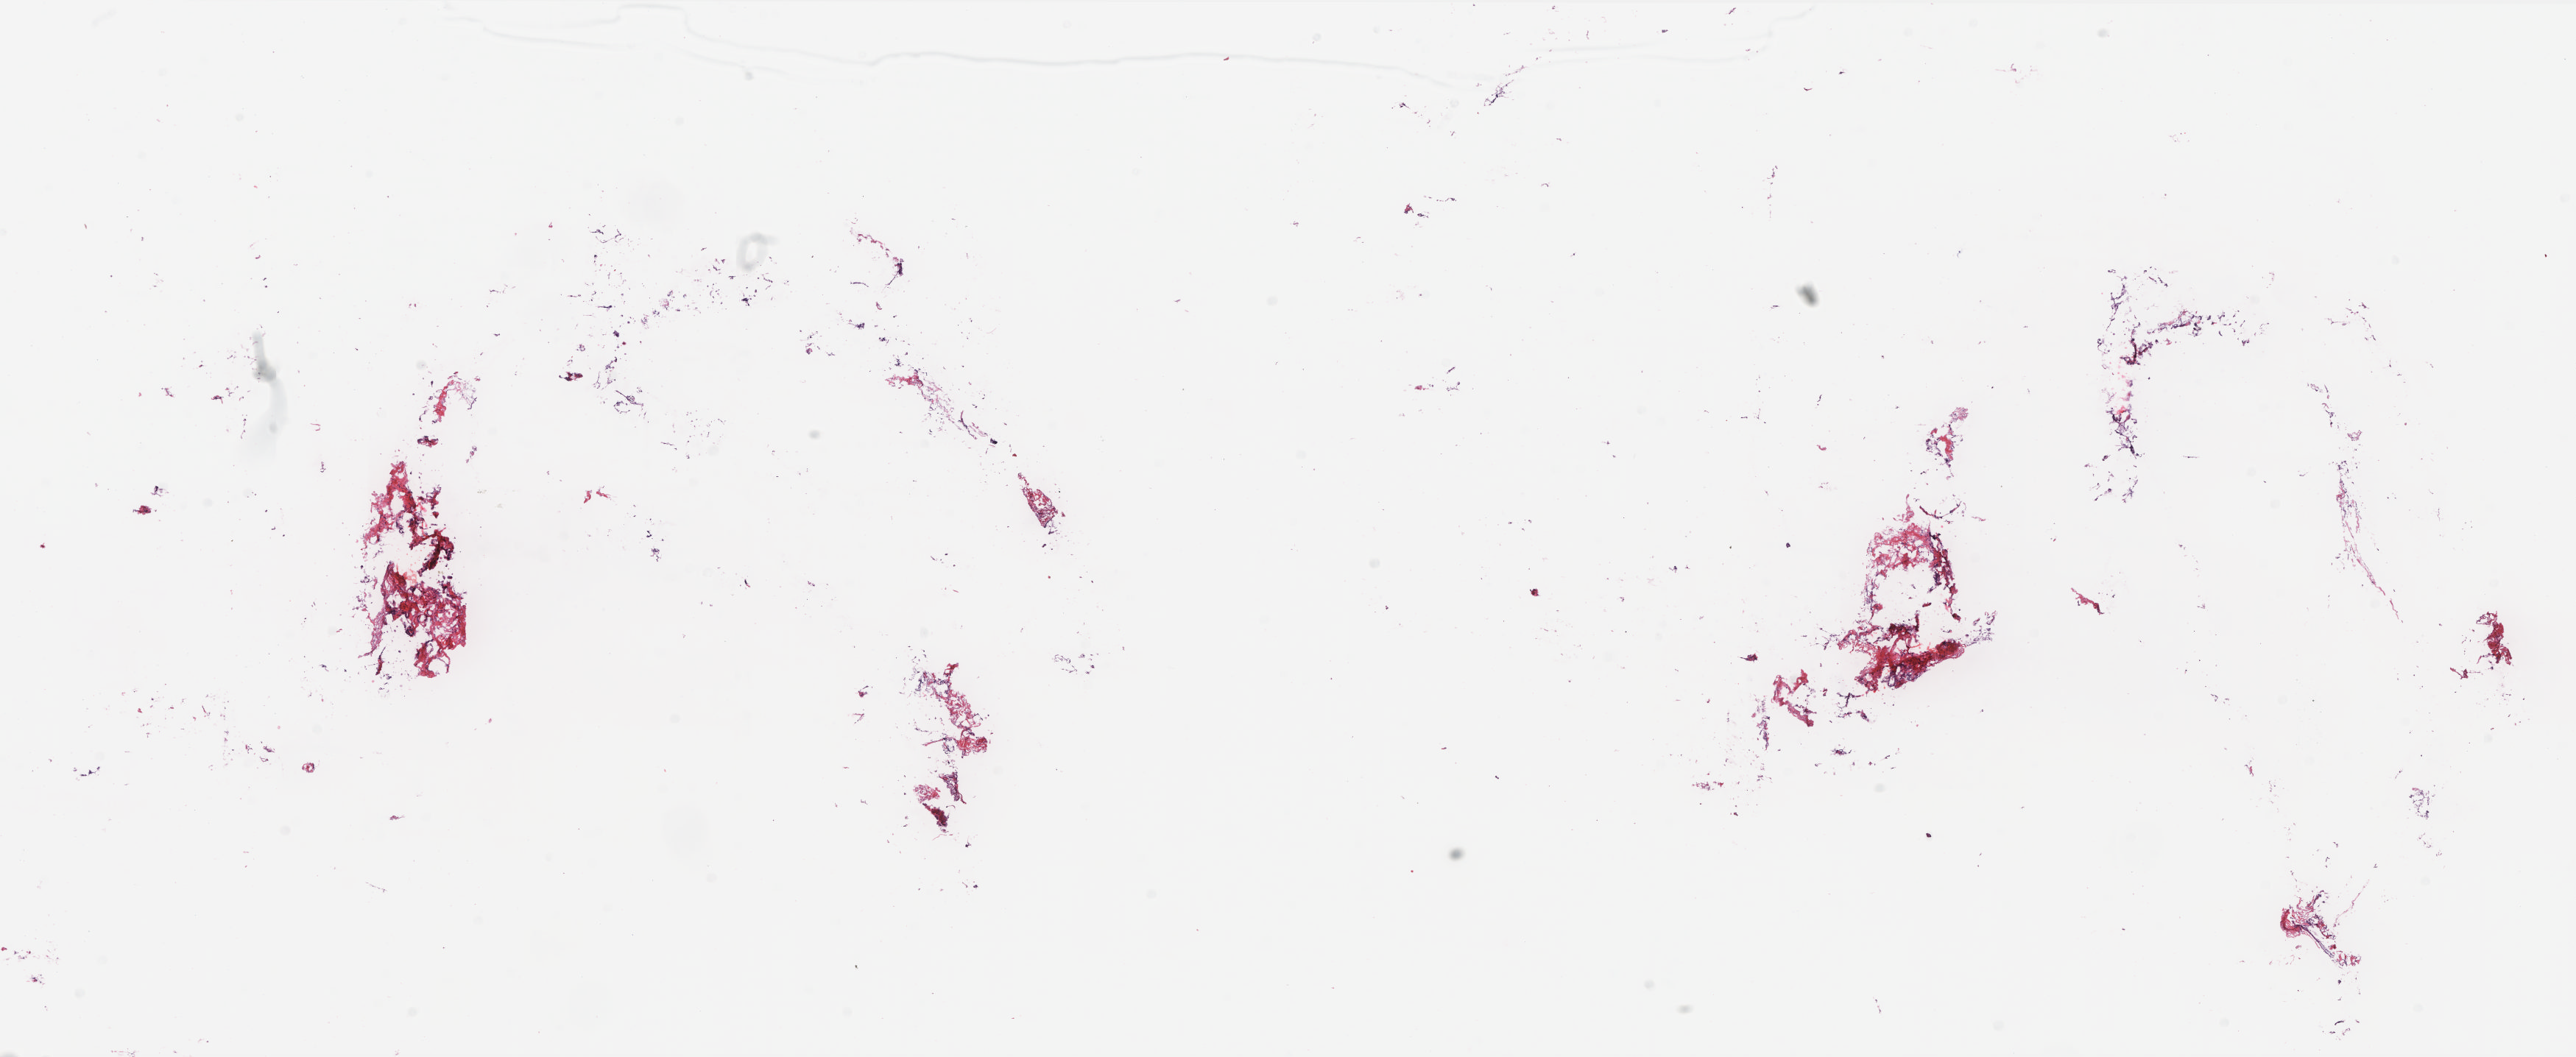
Digitized Hematoxylin and eosin (H&E) stained tissue section (whole slide) — low-resolution overview of the scanned area, about 27.9 x 11.5 mm (acquisition: 20x scan), frozen section, solid tissue normal (non-tumour tissue) sample from the breast. Patient: female, age at initial diagnosis 56 years. Pathologist review of this section (percent, as recorded): tumour cells 0%, tumour nuclei 0%, normal cells 0%, stromal cells 100%, necrosis 0%. Infiltration values recorded for this section: lymphocyte infiltration 1%, monocyte infiltration 0%, neutrophil infiltration 0%.
This section: solid tissue normal (non-tumour) sample from the same patient. Patient diagnosis: Infiltrating duct carcinoma, NOS.